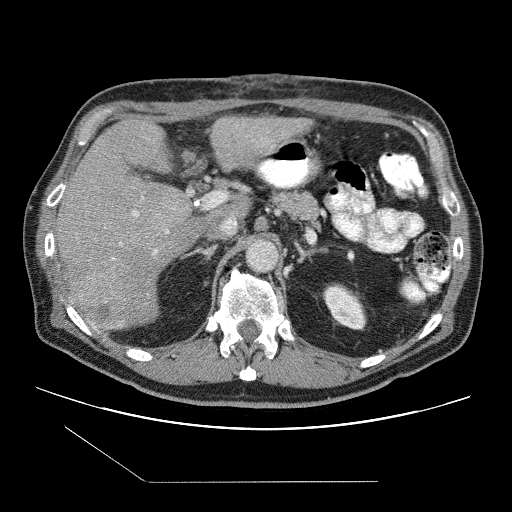
Contrast-enhanced abdominal CT (liver protocol), one axial slice. Slice 55 of 109 in the series (ordered by position). One of 2 acquisitions stored at this slice position. Soft-tissue window (W 400 / L 40 HU). 512 × 512 image matrix. From the clinical record (not read from this slice): diagnosis: hepatocellular carcinoma (patient treated with transarterial chemoembolisation; whether this scan precedes or follows treatment is not stated here); TNM stage (as recorded): Stage-IIIB; Child-Pugh class: A; tumour nodularity: multinodular.
Annotated regions visible in this slice (semi-automatic segmentation, software-assisted and operator-edited):
- liver parenchyma outside the tumour (the mass and vessels are separate outlines, so this box may not span the whole liver): bounding box (x1, y1, x2, y2) in pixels: (54, 116, 310, 328)
- mass: (74, 256, 126, 331)
- liver vessels: (120, 197, 168, 255)